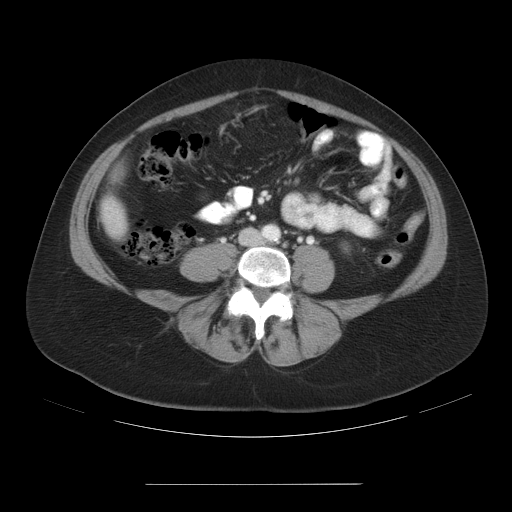
Contrast-enhanced abdominal CT, one axial slice; slice 2 of 27 in the series (ordered by position); reconstruction kernel STANDARD; intravenous contrast given; soft-tissue window (W 400 / L 40 HU); 512 × 512 image matrix, field of view 440 × 440 mm. Female patient, age 58 years. From the clinical record (not read from this slice): diagnosis: colorectal cancer liver metastases, imaged before liver resection; multiple liver metastases: yes; largest metastasis: 1.9 cm; disease in both lobes: yes.
Annotated regions visible in this slice (expert manual segmentation):
- liver: bounding box [x1, y1, x2, y2] px = [108, 203, 112, 221]